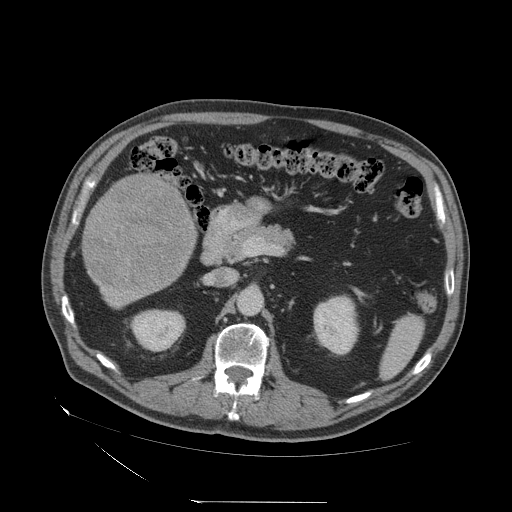
Contrast-enhanced abdominal CT (liver protocol), one axial slice. Slice 15 of 83 in the series (ordered by position). Reconstruction kernel STANDARD. 140 kVp. Soft-tissue window (W 400 / L 40 HU). 2.5 mm slice thickness. 512 × 512 image matrix, field of view 460 × 460 mm. Case-level facts recorded for this patient, not image findings: diagnosis: hepatocellular carcinoma (patient treated with transarterial chemoembolisation; whether this scan precedes or follows treatment is not stated here); TNM stage (as recorded): Stage-I; Child-Pugh class: A; tumour differentiation: well differentiated; tumour nodularity: uninodular.
Outlined on this slice (semi-automatic segmentation, software-assisted and operator-edited):
- liver parenchyma outside the tumour (the mass and vessels are separate outlines, so this box may not span the whole liver): box from (x=84, y=174) to (x=196, y=307) px
- mass: (x=85, y=177)–(x=193, y=289)